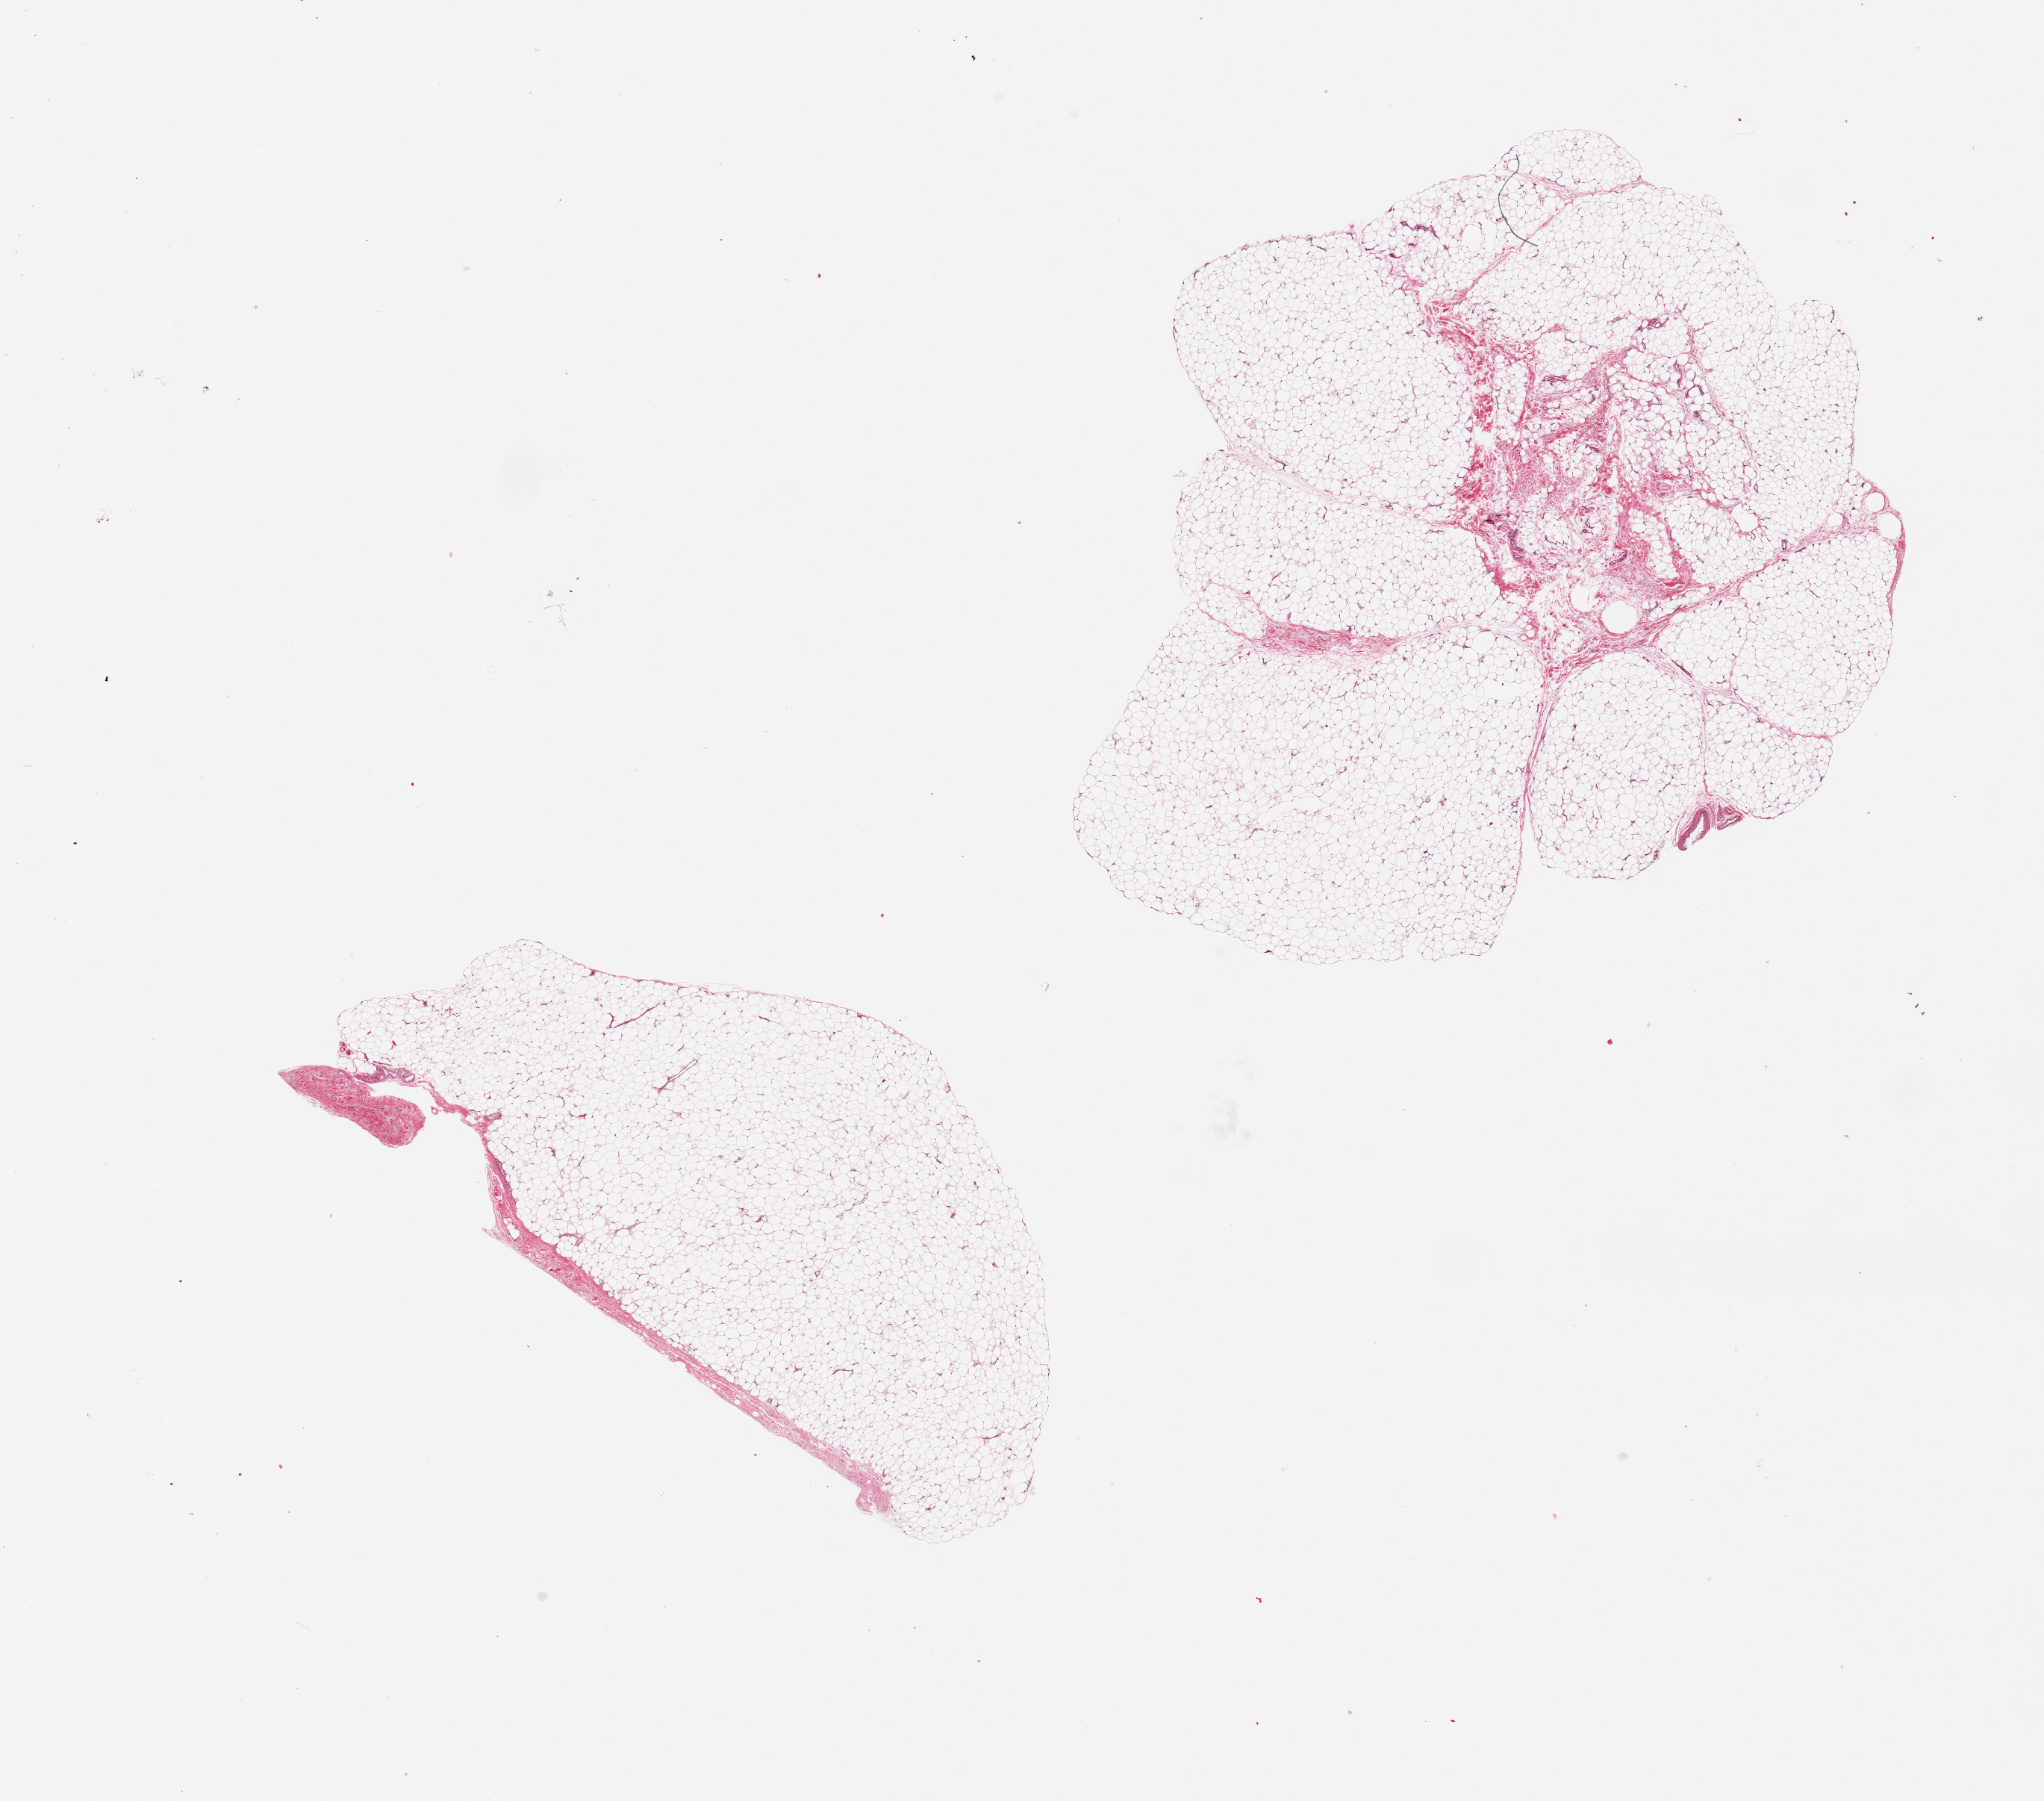
Haematoxylin and eosin whole-slide image, brightfield, whole scanned area (about 21.7 x 19.1 mm) shown as a low-resolution overview, PAXgene-fixed, paraffin-embedded tissue, section of adipose tissue (target tissue), donor tissue sample. Donor sex: female.
Pathologist's review note for this sample: 2 pieces.